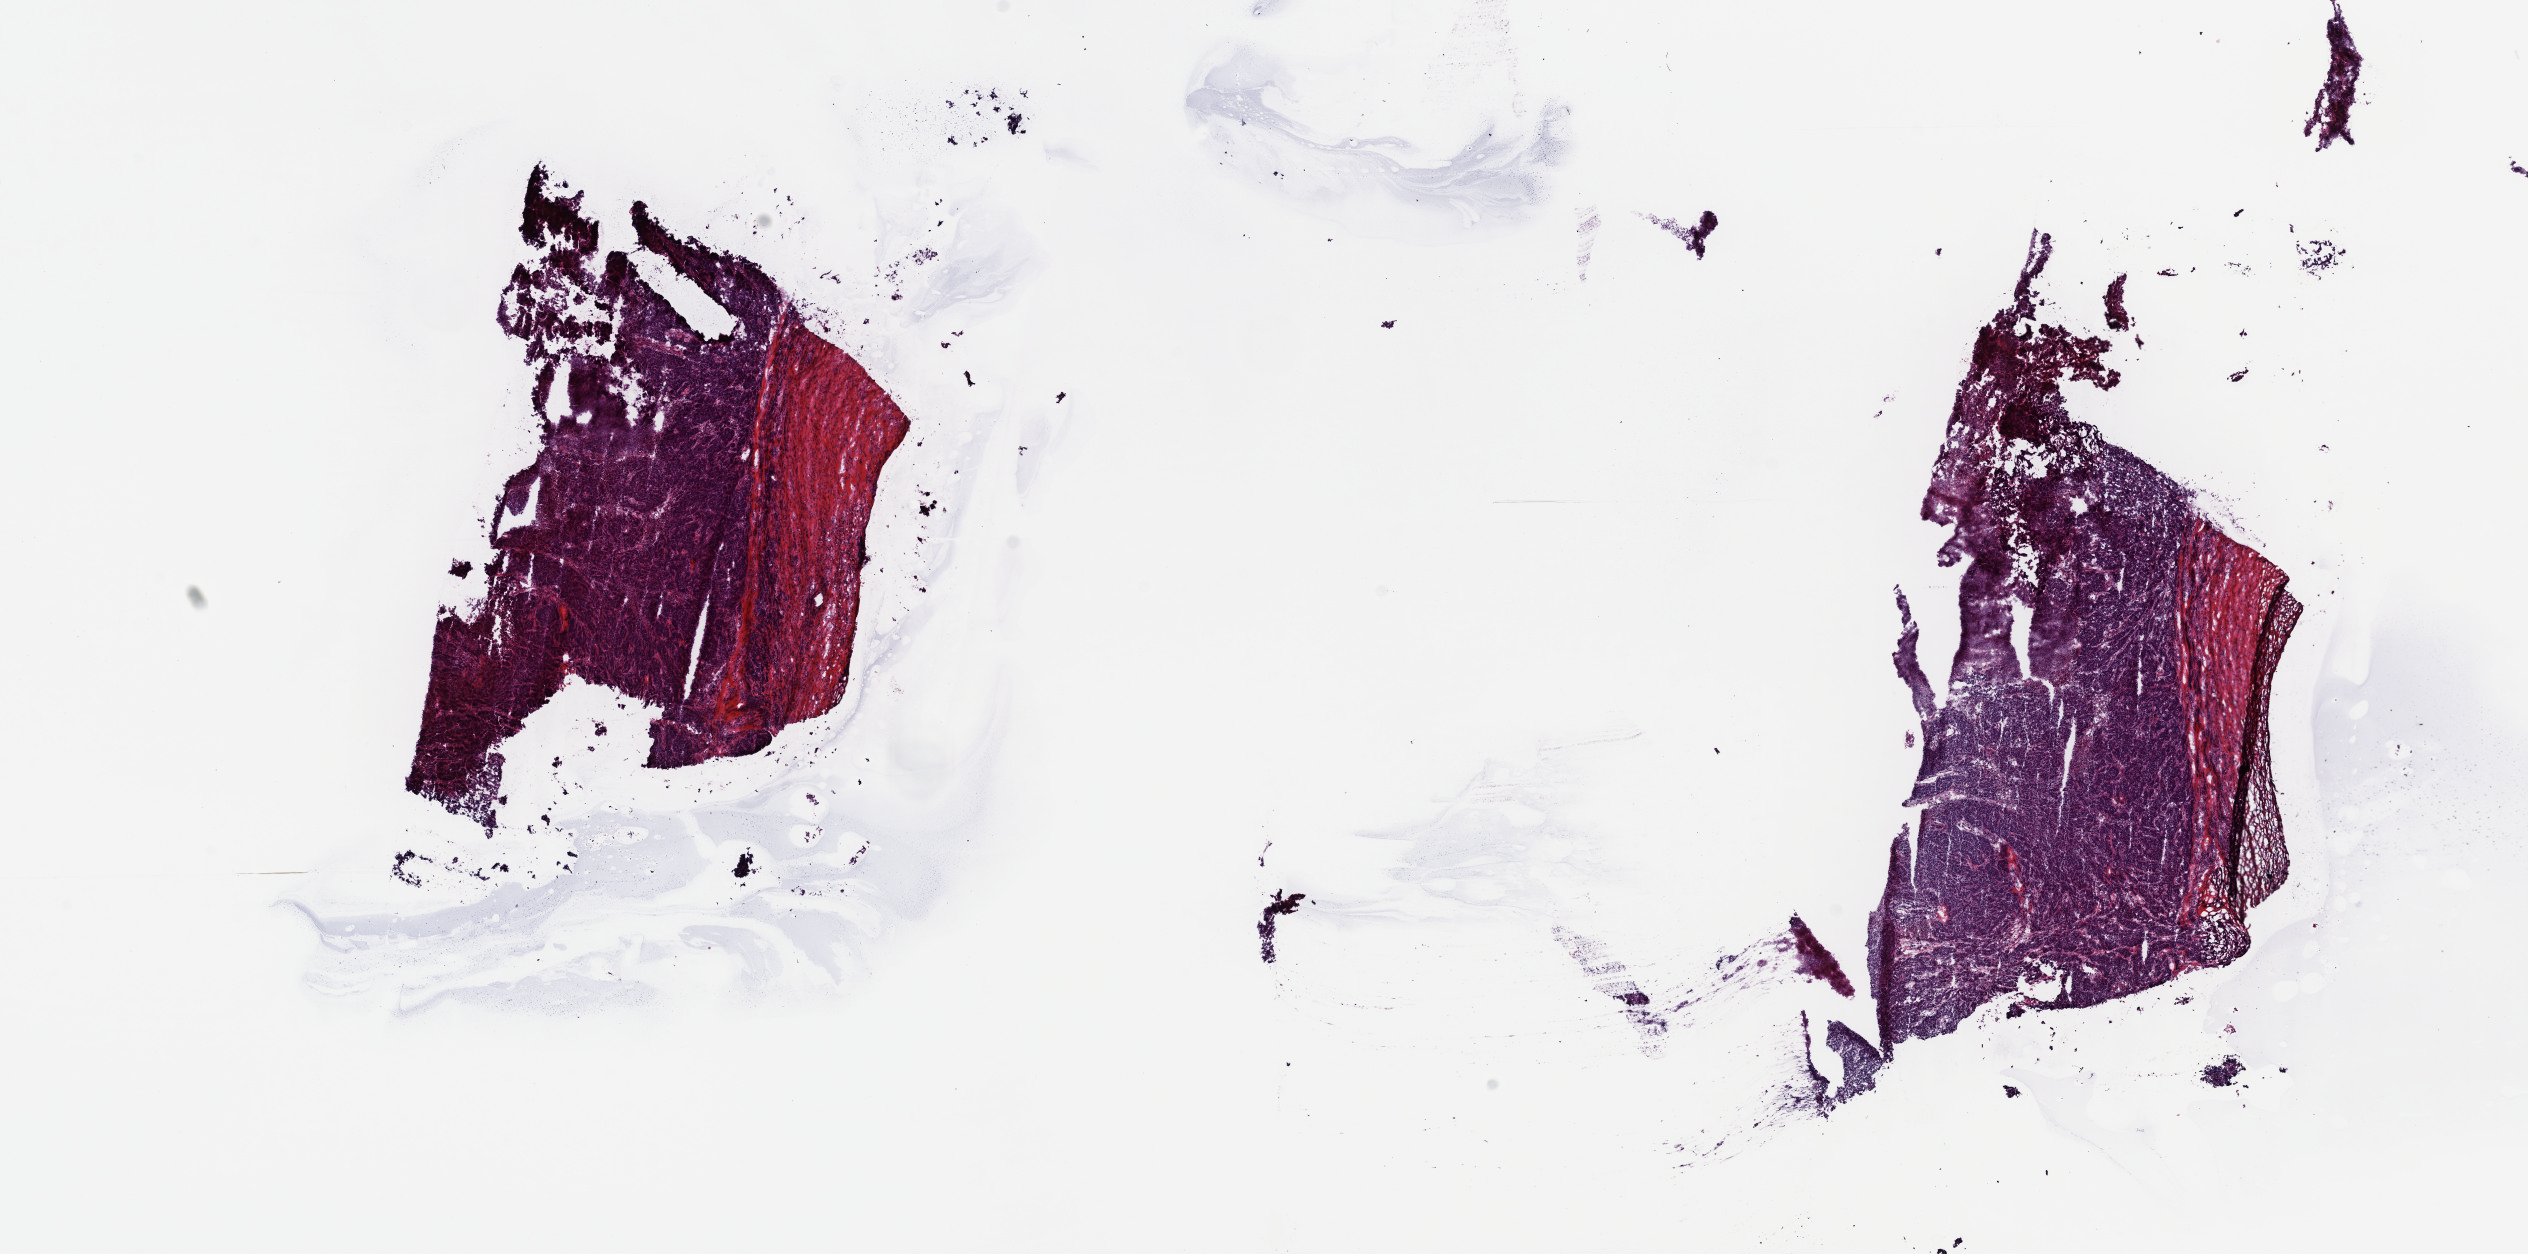
Hematoxylin and eosin (H&E) stained whole-slide image, low-resolution overview of the scanned area, about 19.9 x 9.9 mm (slide scanned at 40x), frozen section from the top of the tissue portion, sample: primary tumour, breast. Female patient; age at initial diagnosis 55 years. Composition of this section per pathologist review: tumour cells 60%, tumour nuclei 90%, normal cells 0%, stromal cells 20%, necrosis 20%. Infiltration values recorded for this section: lymphocyte infiltration 1%, monocyte infiltration 0%, neutrophil infiltration 0%.
AJCC pathologic stage: IIB (7th edition). Laterality: left. Pathologic diagnosis: Infiltrating duct carcinoma, NOS.